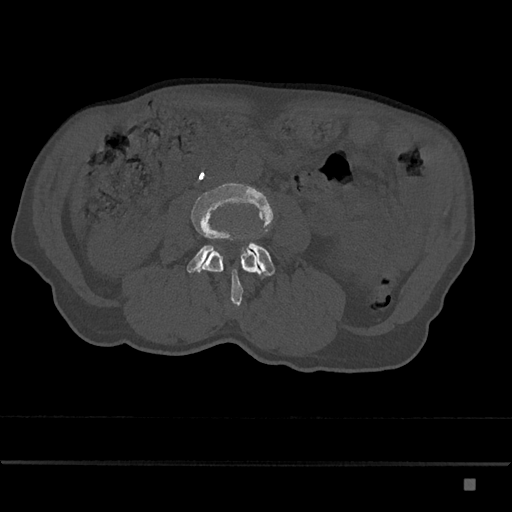
CT including the spine, one axial slice. Slice 377 of 797 in the series (ordered by position). Reconstruction kernel Br40s/3. 120 kVp. Bone window (W 1800 / L 400 HU). 0.5 mm slice thickness. 512 × 512 image matrix, field of view 390 × 390 mm. Male patient, age 72 years. Case-level facts recorded for this patient, not image findings: primary cancer: prostate.
Structures marked on this image (semi-automatic segmentation, software-assisted and operator-edited):
- L3 vertebra: bounding box (x1, y1, x2, y2) in pixels: (191, 182, 274, 307)
- L4 vertebra: (187, 242, 275, 279)